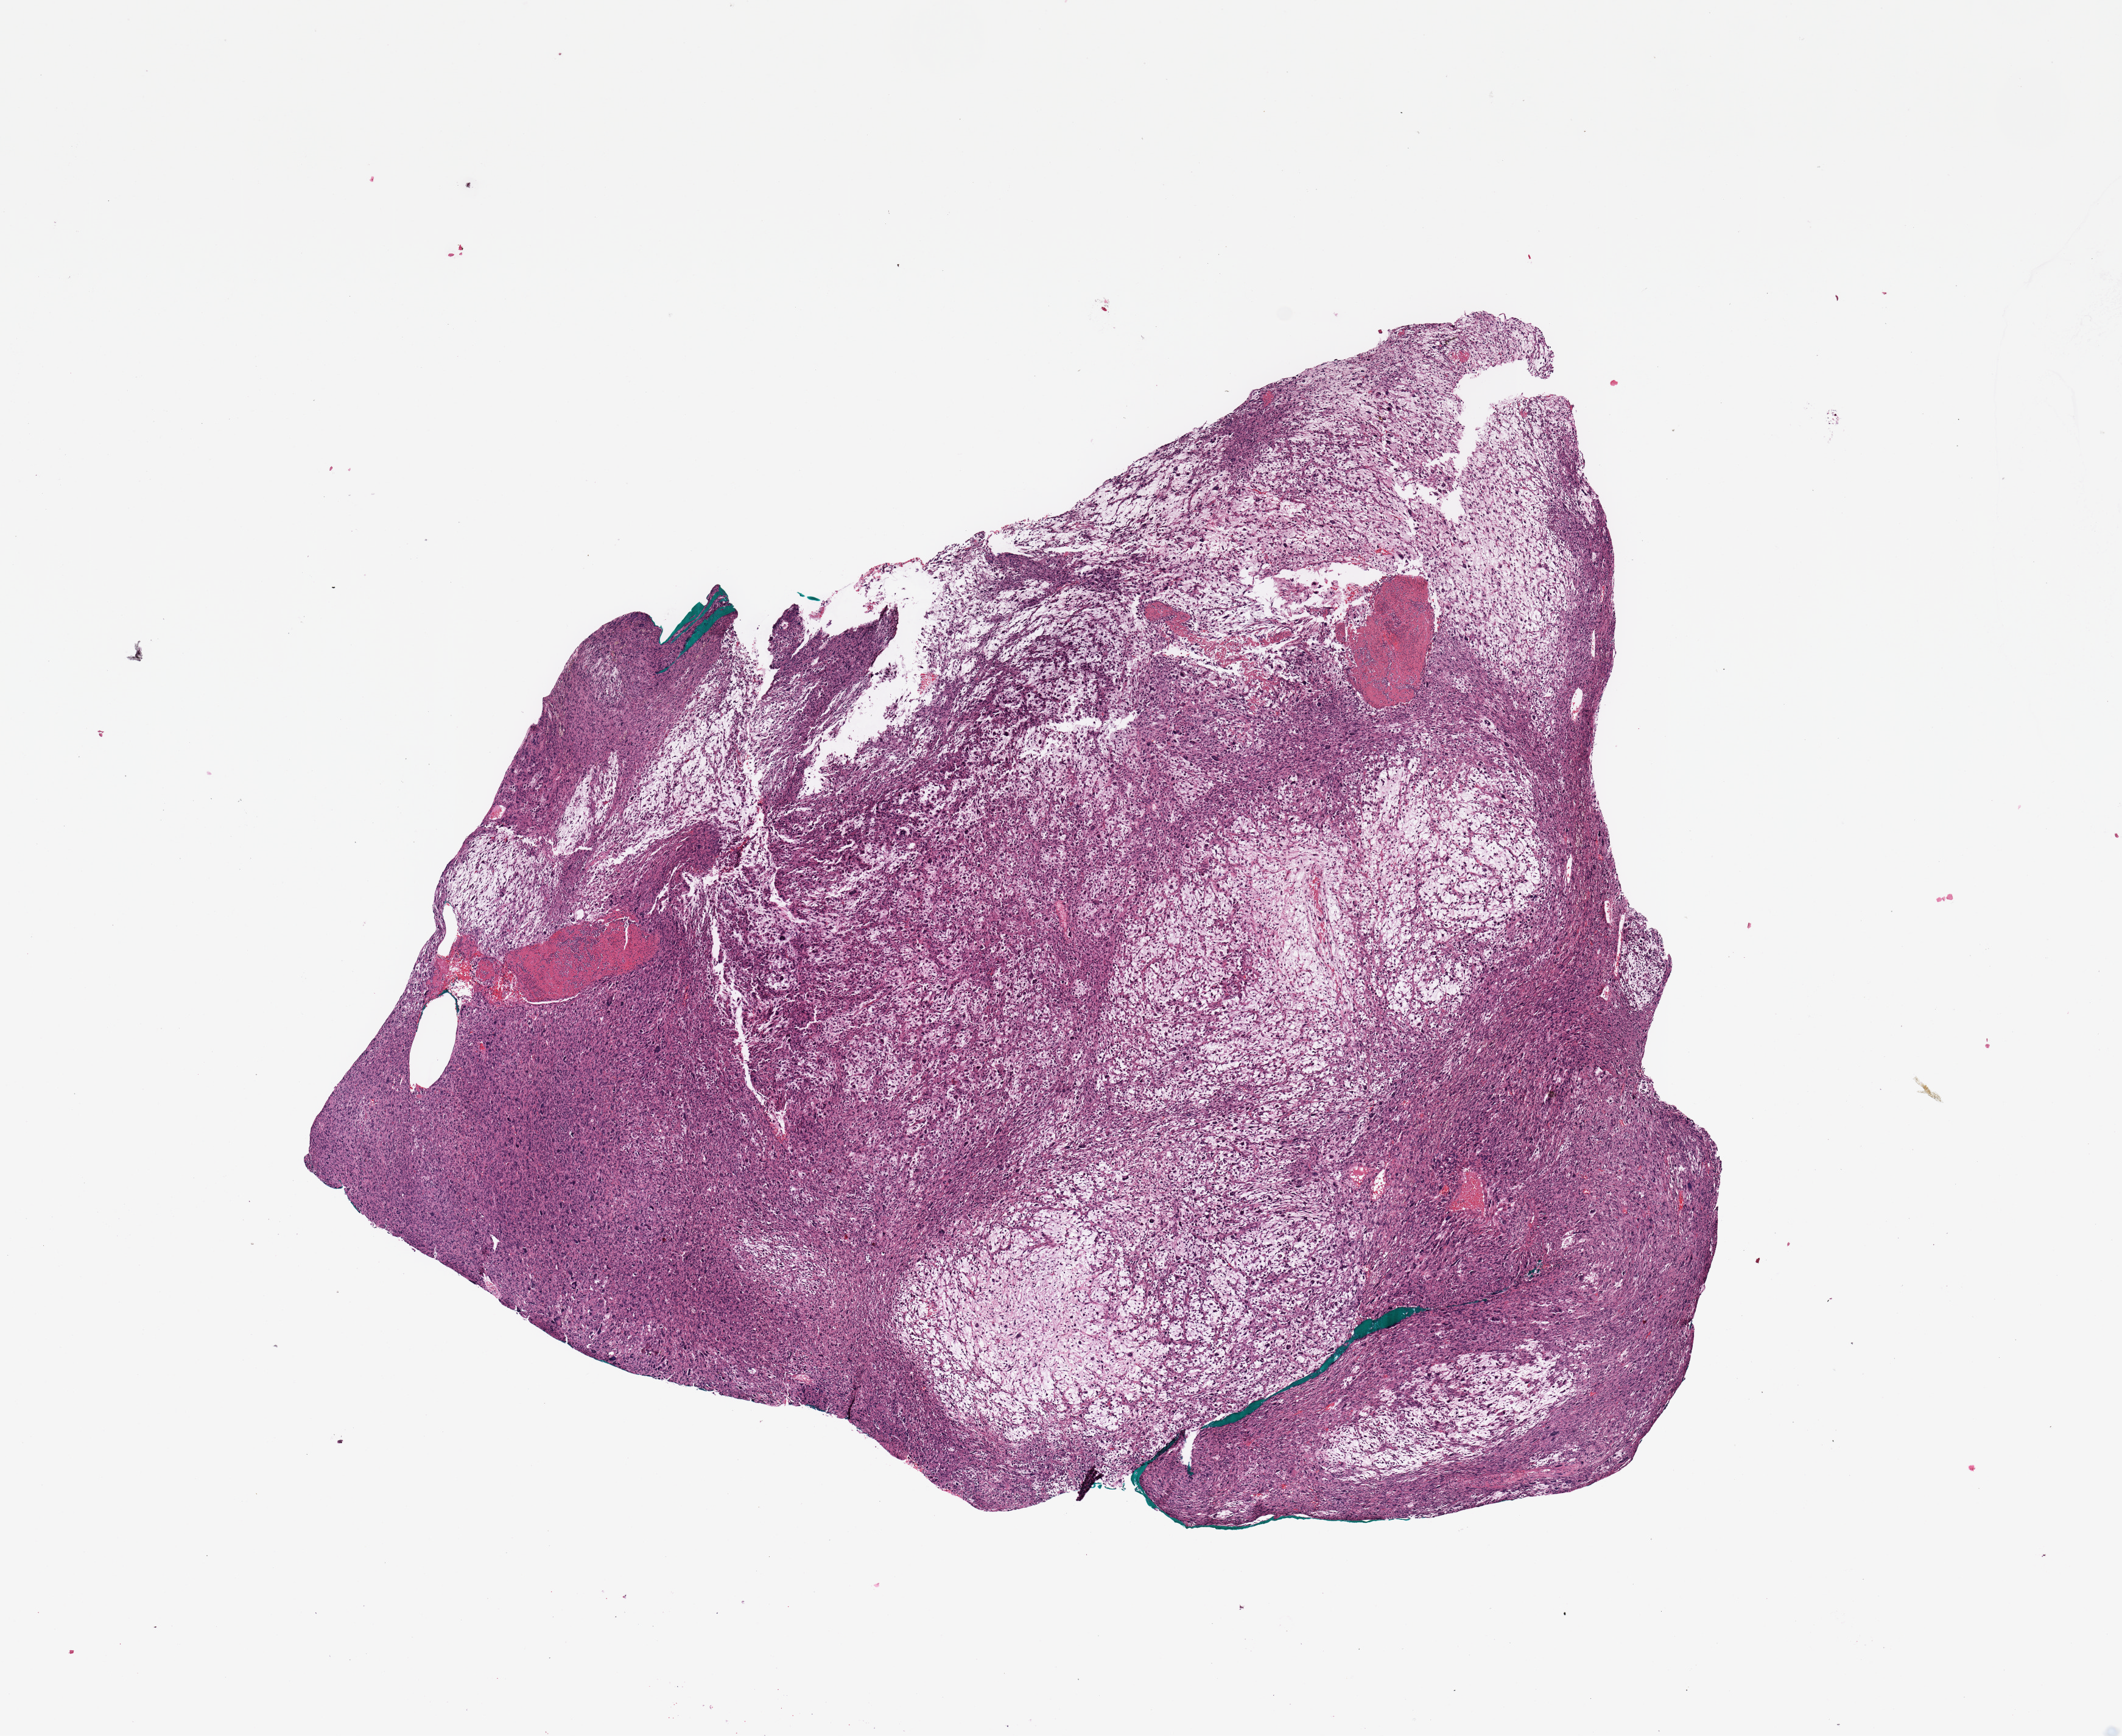
Digitized Hematoxylin and eosin (H&E) stained tissue section (whole slide), low-resolution overview of the scanned area, about 13.8 x 11.3 mm; tumour tissue sample. Female, 62 y/o.
* patient diagnosis (cohort enrolment): sarcoma (site not recorded at cohort level)
* primary tumour site (as recorded): lower extremity